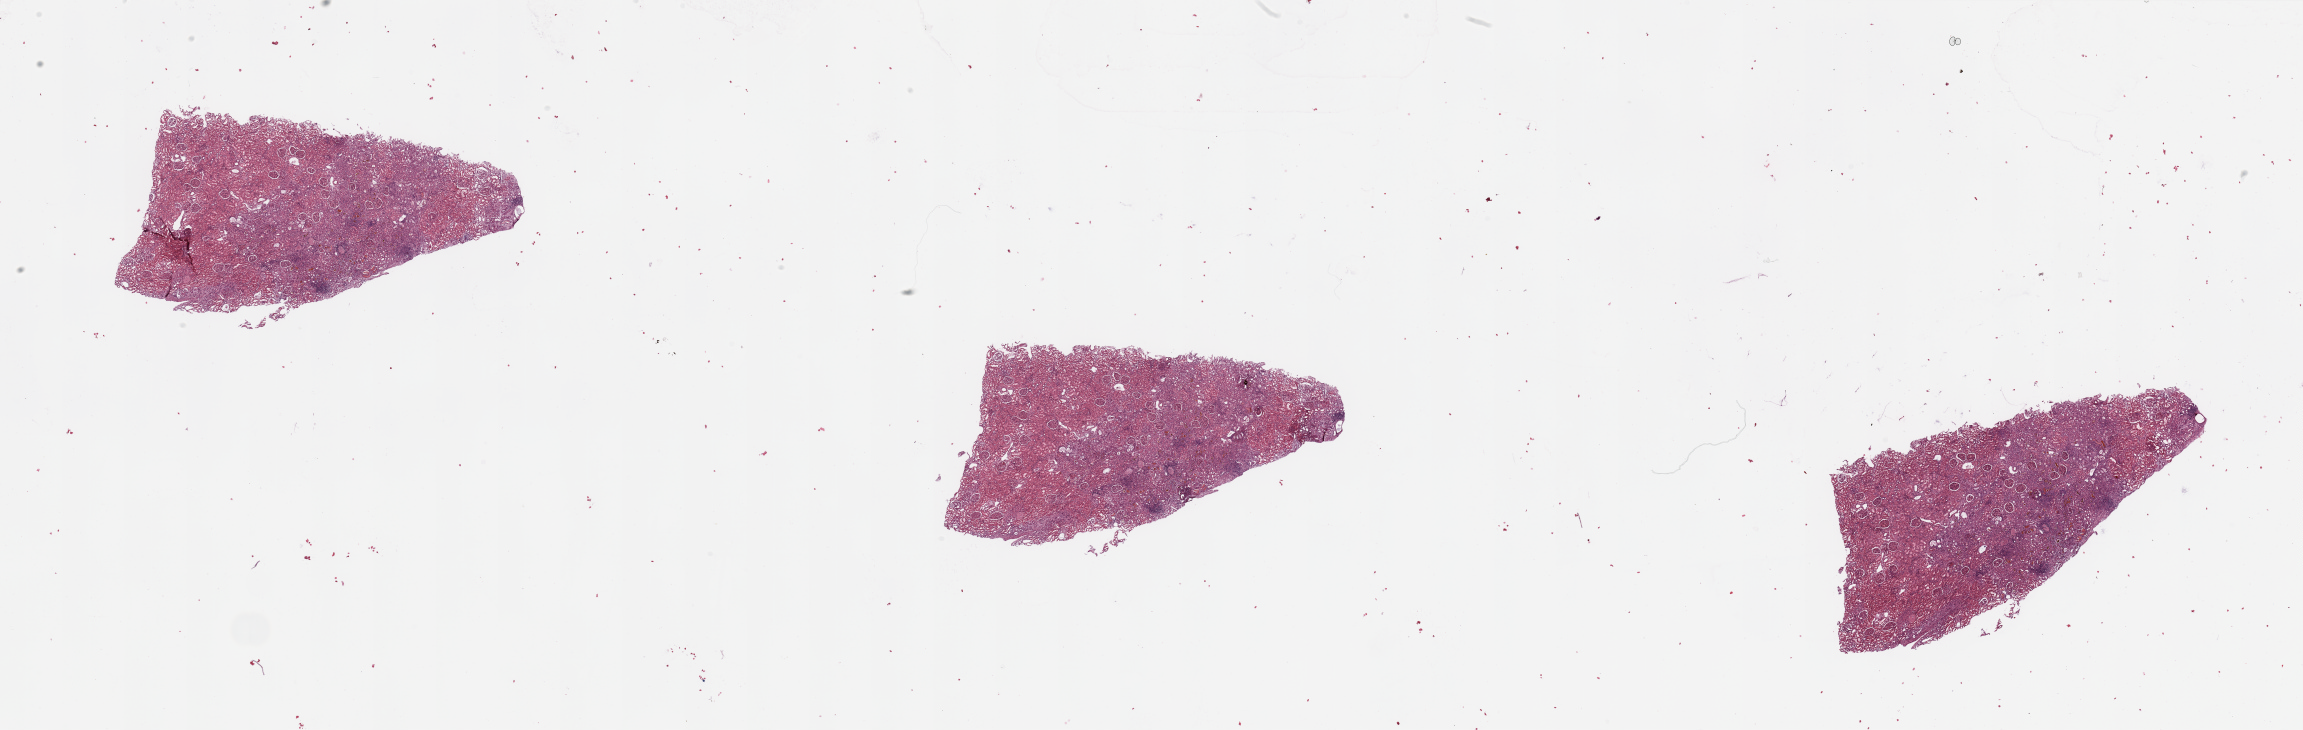
H&E-stained whole-slide image — shown as a low-resolution overview of the whole scanned area (about 36.4 x 11.5 mm, from a 20x scan). Normal (non-tumour) tissue sample, sampled site: kidney. 58-year-old male patient.
- this section: normal (non-tumour) tissue from the same patient
- patient diagnosis: Renal cell carcinoma, NOS